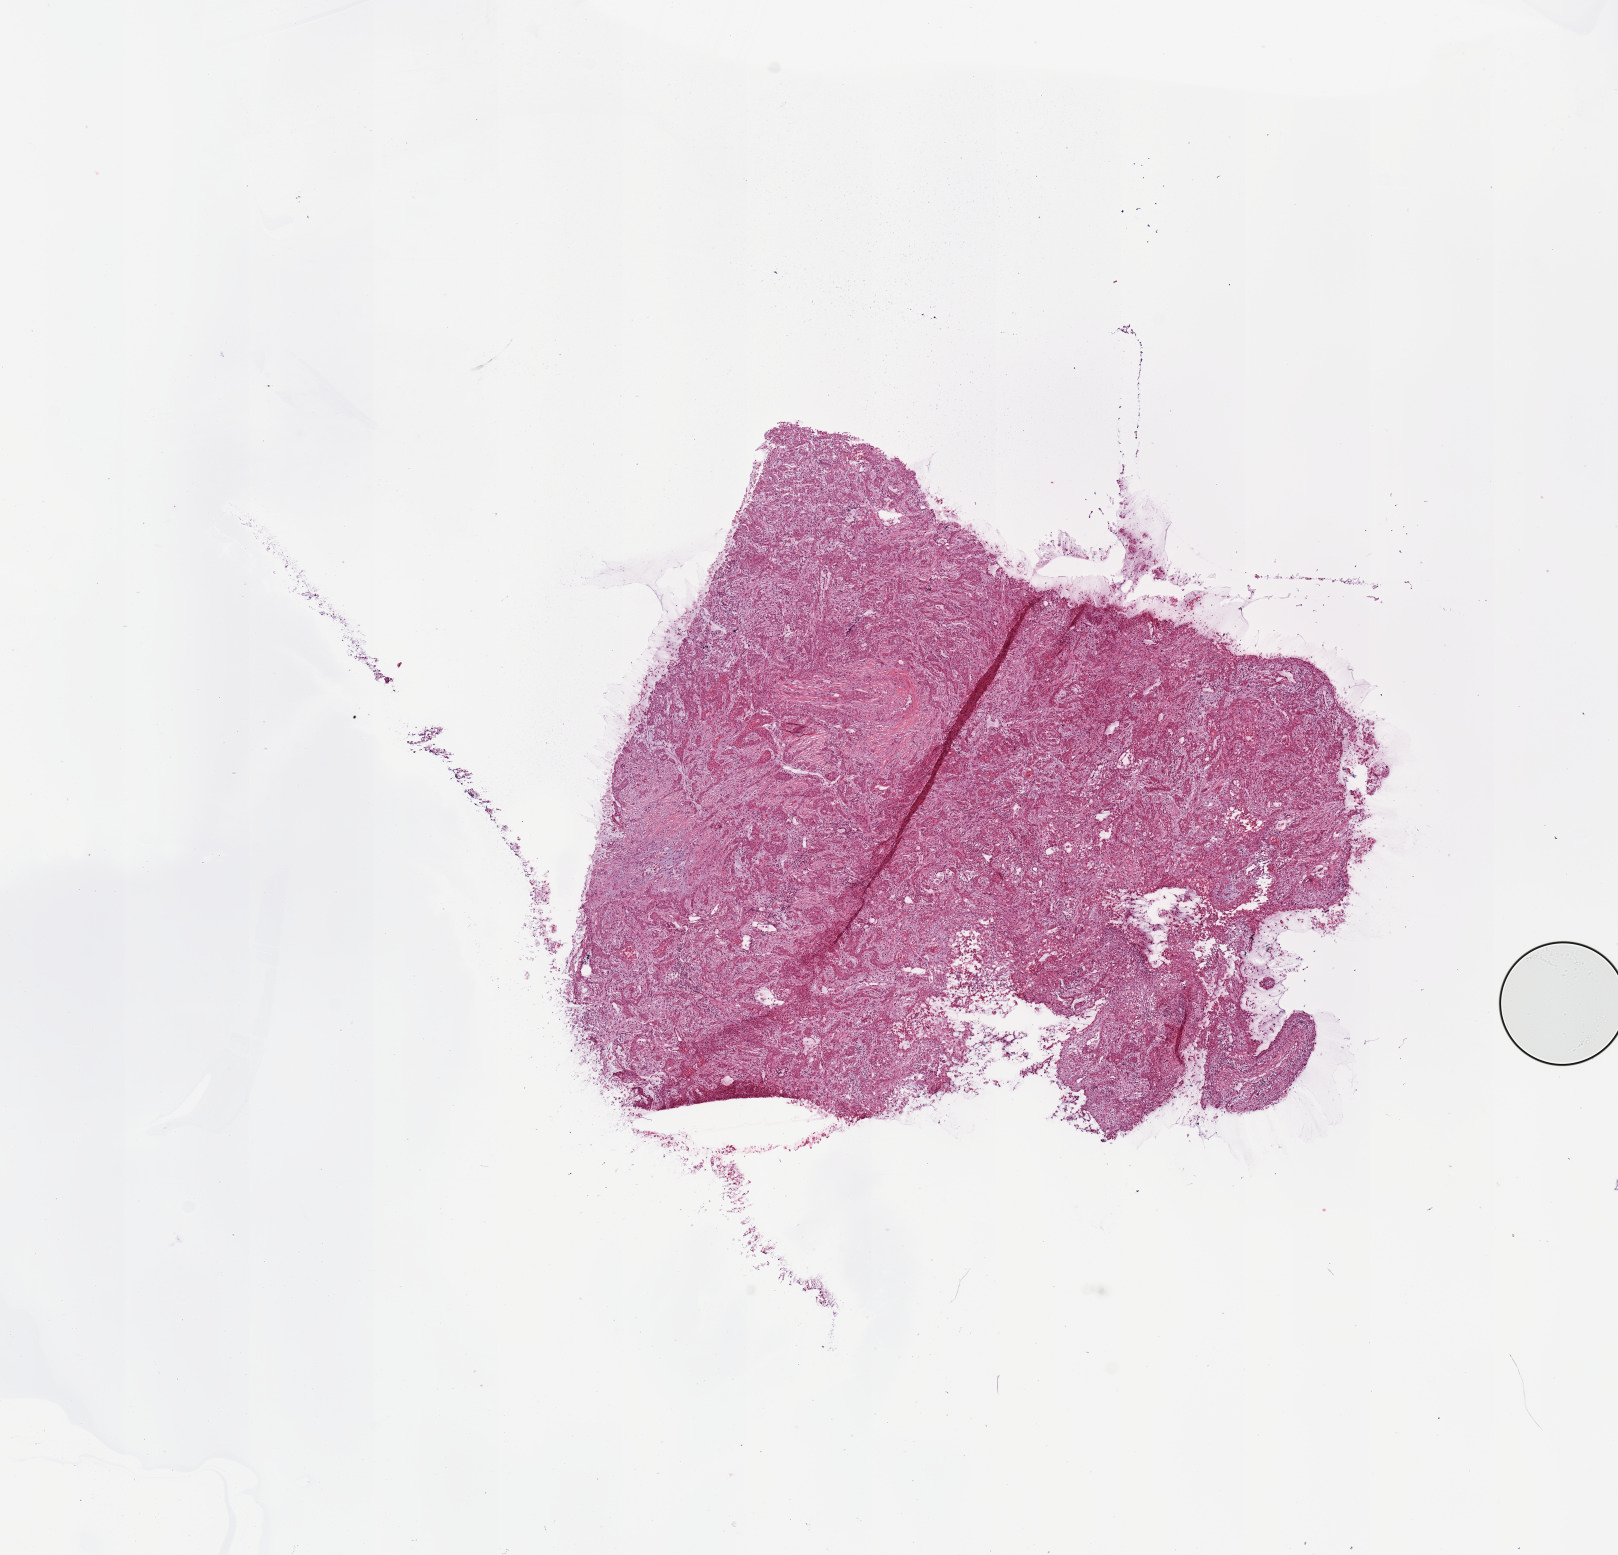
Whole-slide histology image, H&E — a low-resolution overview of the entire scanned area, about 12.8 x 12.3 mm. Tumour tissue sample, lung. Female, 75 y/o.
• primary tumour site (as recorded): right upper lobe
• patient diagnosis (cohort enrolment): squamous cell carcinoma (lung)